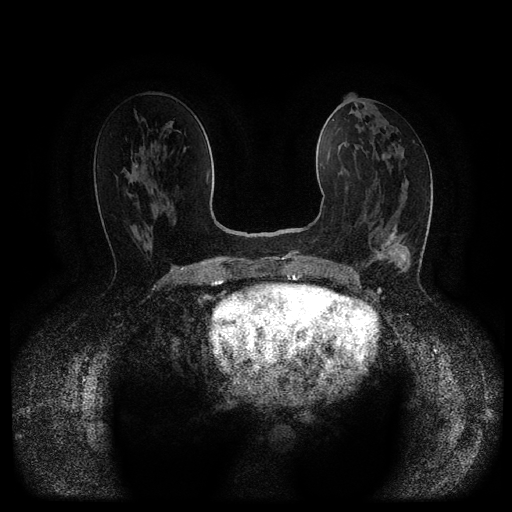
Breast MRI (dynamic contrast-enhanced, multi-phase), one axial slice. Position 49 of 116 along the scan axis. Dynamic contrast-enhanced series, time point 2 of 5 at this slice position (early post-contrast). 1.5 T. TE 2.6 ms, TR 5.4 ms. 2 mm slice thickness. 512 × 512 image matrix, field of view 340 × 340 mm. Patient: female, 61 years.
Annotated regions visible in this slice (semi-automatically segmented with operator editing):
- breast lesion (labelled 'tumour' in the annotation; benign lesions carry a separate 'benign' label): bounding box <374,225,398,261> (left, top, right, bottom; pixels)